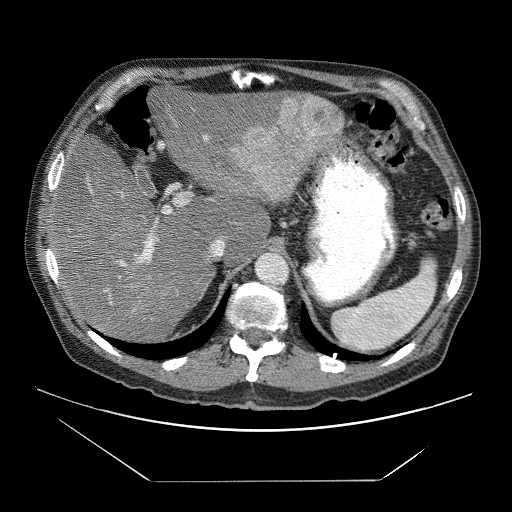
Contrast-enhanced abdominal CT (liver protocol), one axial slice; slice 46 of 83 in the series (ordered by position); reconstruction kernel STANDARD; soft-tissue window (W 400 / L 40 HU); 2.5 mm slice thickness; 512 × 512 image matrix, field of view 420 × 420 mm. From the clinical record (not read from this slice): diagnosis: hepatocellular carcinoma (patient treated with transarterial chemoembolisation; whether this scan precedes or follows treatment is not stated here); TNM stage (as recorded): Stage-IVB; Child-Pugh class: B.
Outlined on this slice (semi-automatic segmentation, software-assisted and operator-edited):
- liver parenchyma outside the tumour (the mass and vessels are separate outlines, so this box may not span the whole liver): box from (x=52, y=79) to (x=342, y=340) px
- mass: (x=230, y=93)–(x=343, y=198)
- liver vessels: (x=89, y=135)–(x=316, y=304)